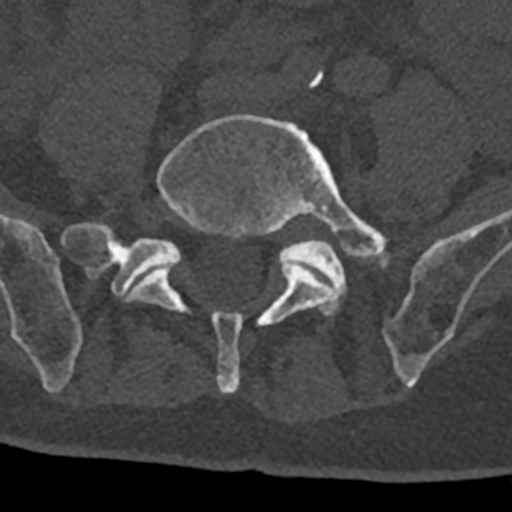
CT including the spine, one axial slice. Reconstruction kernel Br40s/3. 120 kVp. Bone window (W 1800 / L 400 HU). 0.5 mm slice thickness. 512 × 512 image matrix, field of view 160 × 160 mm. Male patient, age 74 years. From the clinical record (not read from this slice): primary cancer: renal.
Outlined on this slice (semi-automatically segmented with operator editing):
- L4 vertebra: bounding box (x1, y1, x2, y2) in pixels: (315, 71, 324, 87)
- L5 vertebra: (127, 115, 387, 393)